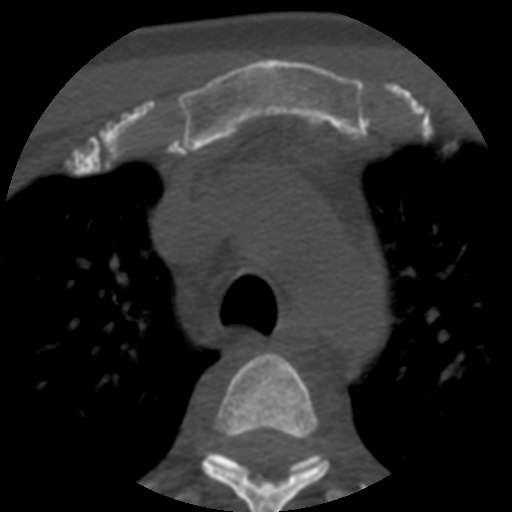
CT including the spine, one axial slice; position 409 of 508 along the scan axis; reconstruction kernel STANDARD; 120 kVp; bone window (W 1800 / L 400 HU); 512 × 512 image matrix, field of view 160 × 160 mm. Patient age 57 years. Case-level facts recorded for this patient, not image findings: primary cancer: prostate.
Outlined on this slice (semi-automatically segmented with operator editing):
- T3 vertebra: bounding box [x1, y1, x2, y2] px = [202, 353, 328, 512]
- T4 vertebra: [180, 452, 344, 499]